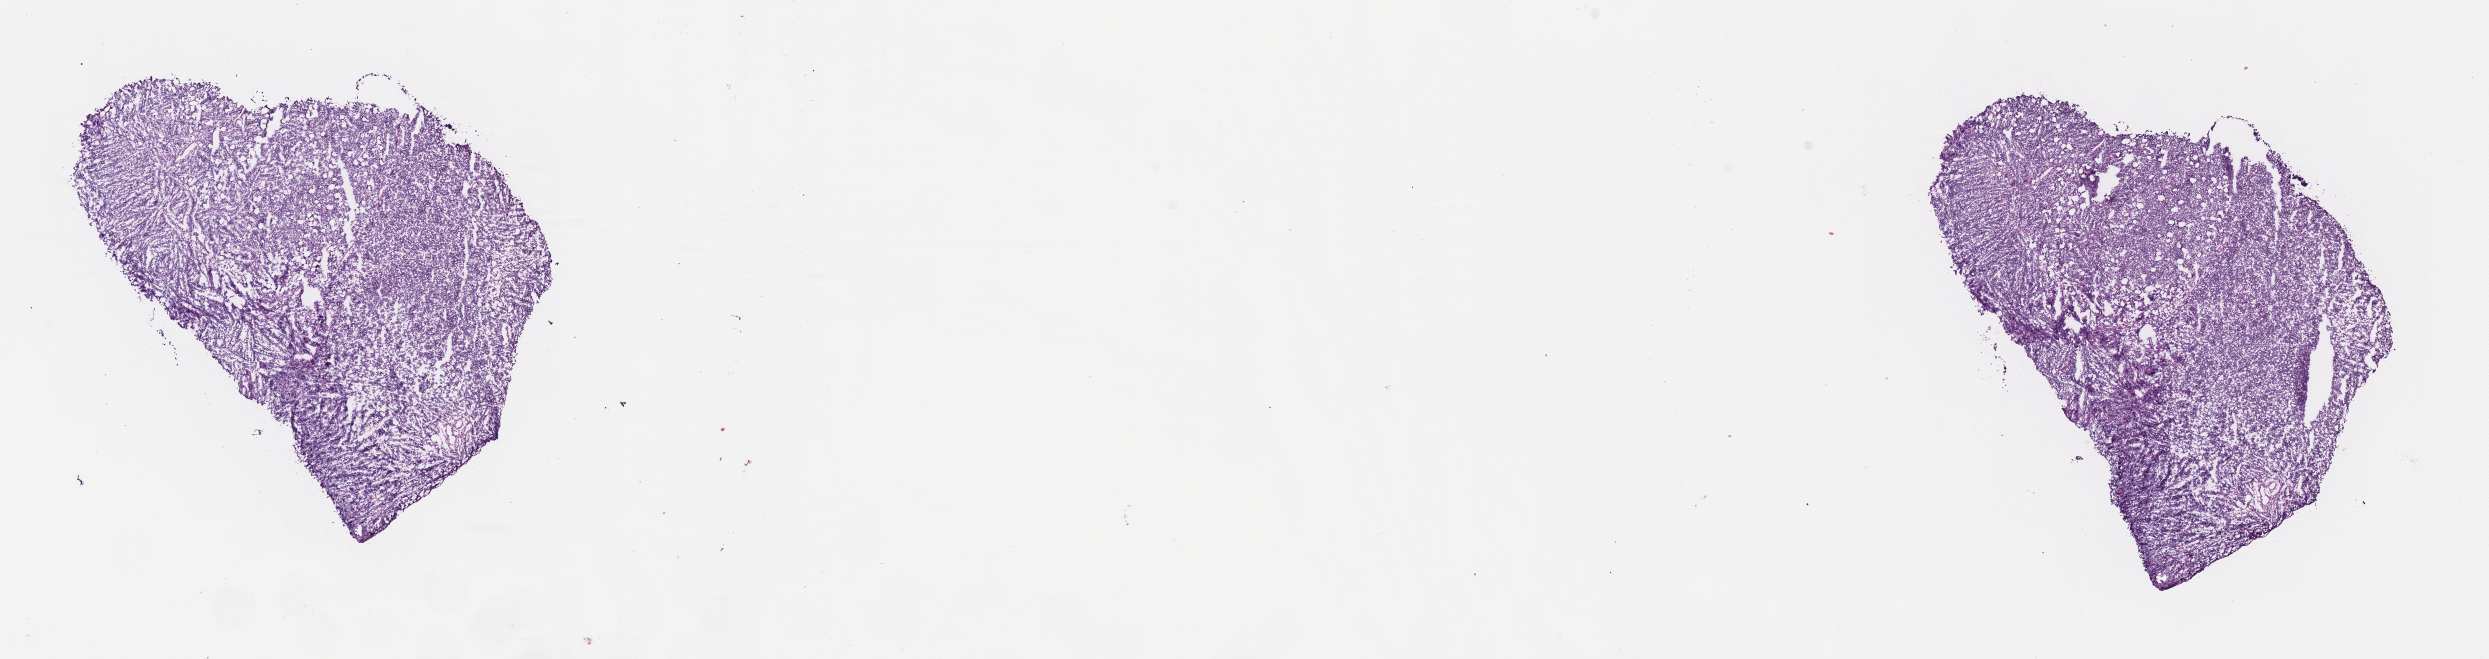
Hematoxylin and eosin (H&E) whole-slide image, a low-resolution overview of the entire scanned area, about 20.1 x 5.3 mm. Cryosection. Primary tumor. Anatomic site: abdominal lymph node. Female patient, age 14 years. Slide review estimates, as recorded: tumor cells 90%, tumor nuclei 95%, stromal cells 5%, necrosis 5%, normal cells 0%. Infiltration values recorded for this section: lymphocyte infiltration 3%, monocyte infiltration 3%, neutrophil infiltration 0%.
• section: bottom of the tissue portion
• diagnosis: Burkitt lymphoma, NOS
• Ann Arbor stage (patient): Stage III